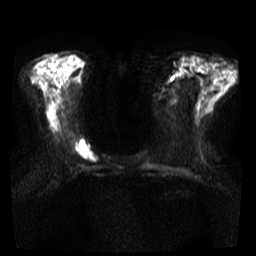
Breast MRI, one axial slice. Position 12 of 35 along the scan axis. Diffusion-weighted series; image 2 of 4 stored at this slice position (different b-values; order by instance number). 3 T. 5 mm slice thickness. 256 × 256 image matrix. Female patient.
Outlined on this slice (manually delineated by an expert):
- tumour on diffusion-weighted imaging: box from (x=74, y=141) to (x=96, y=163) px